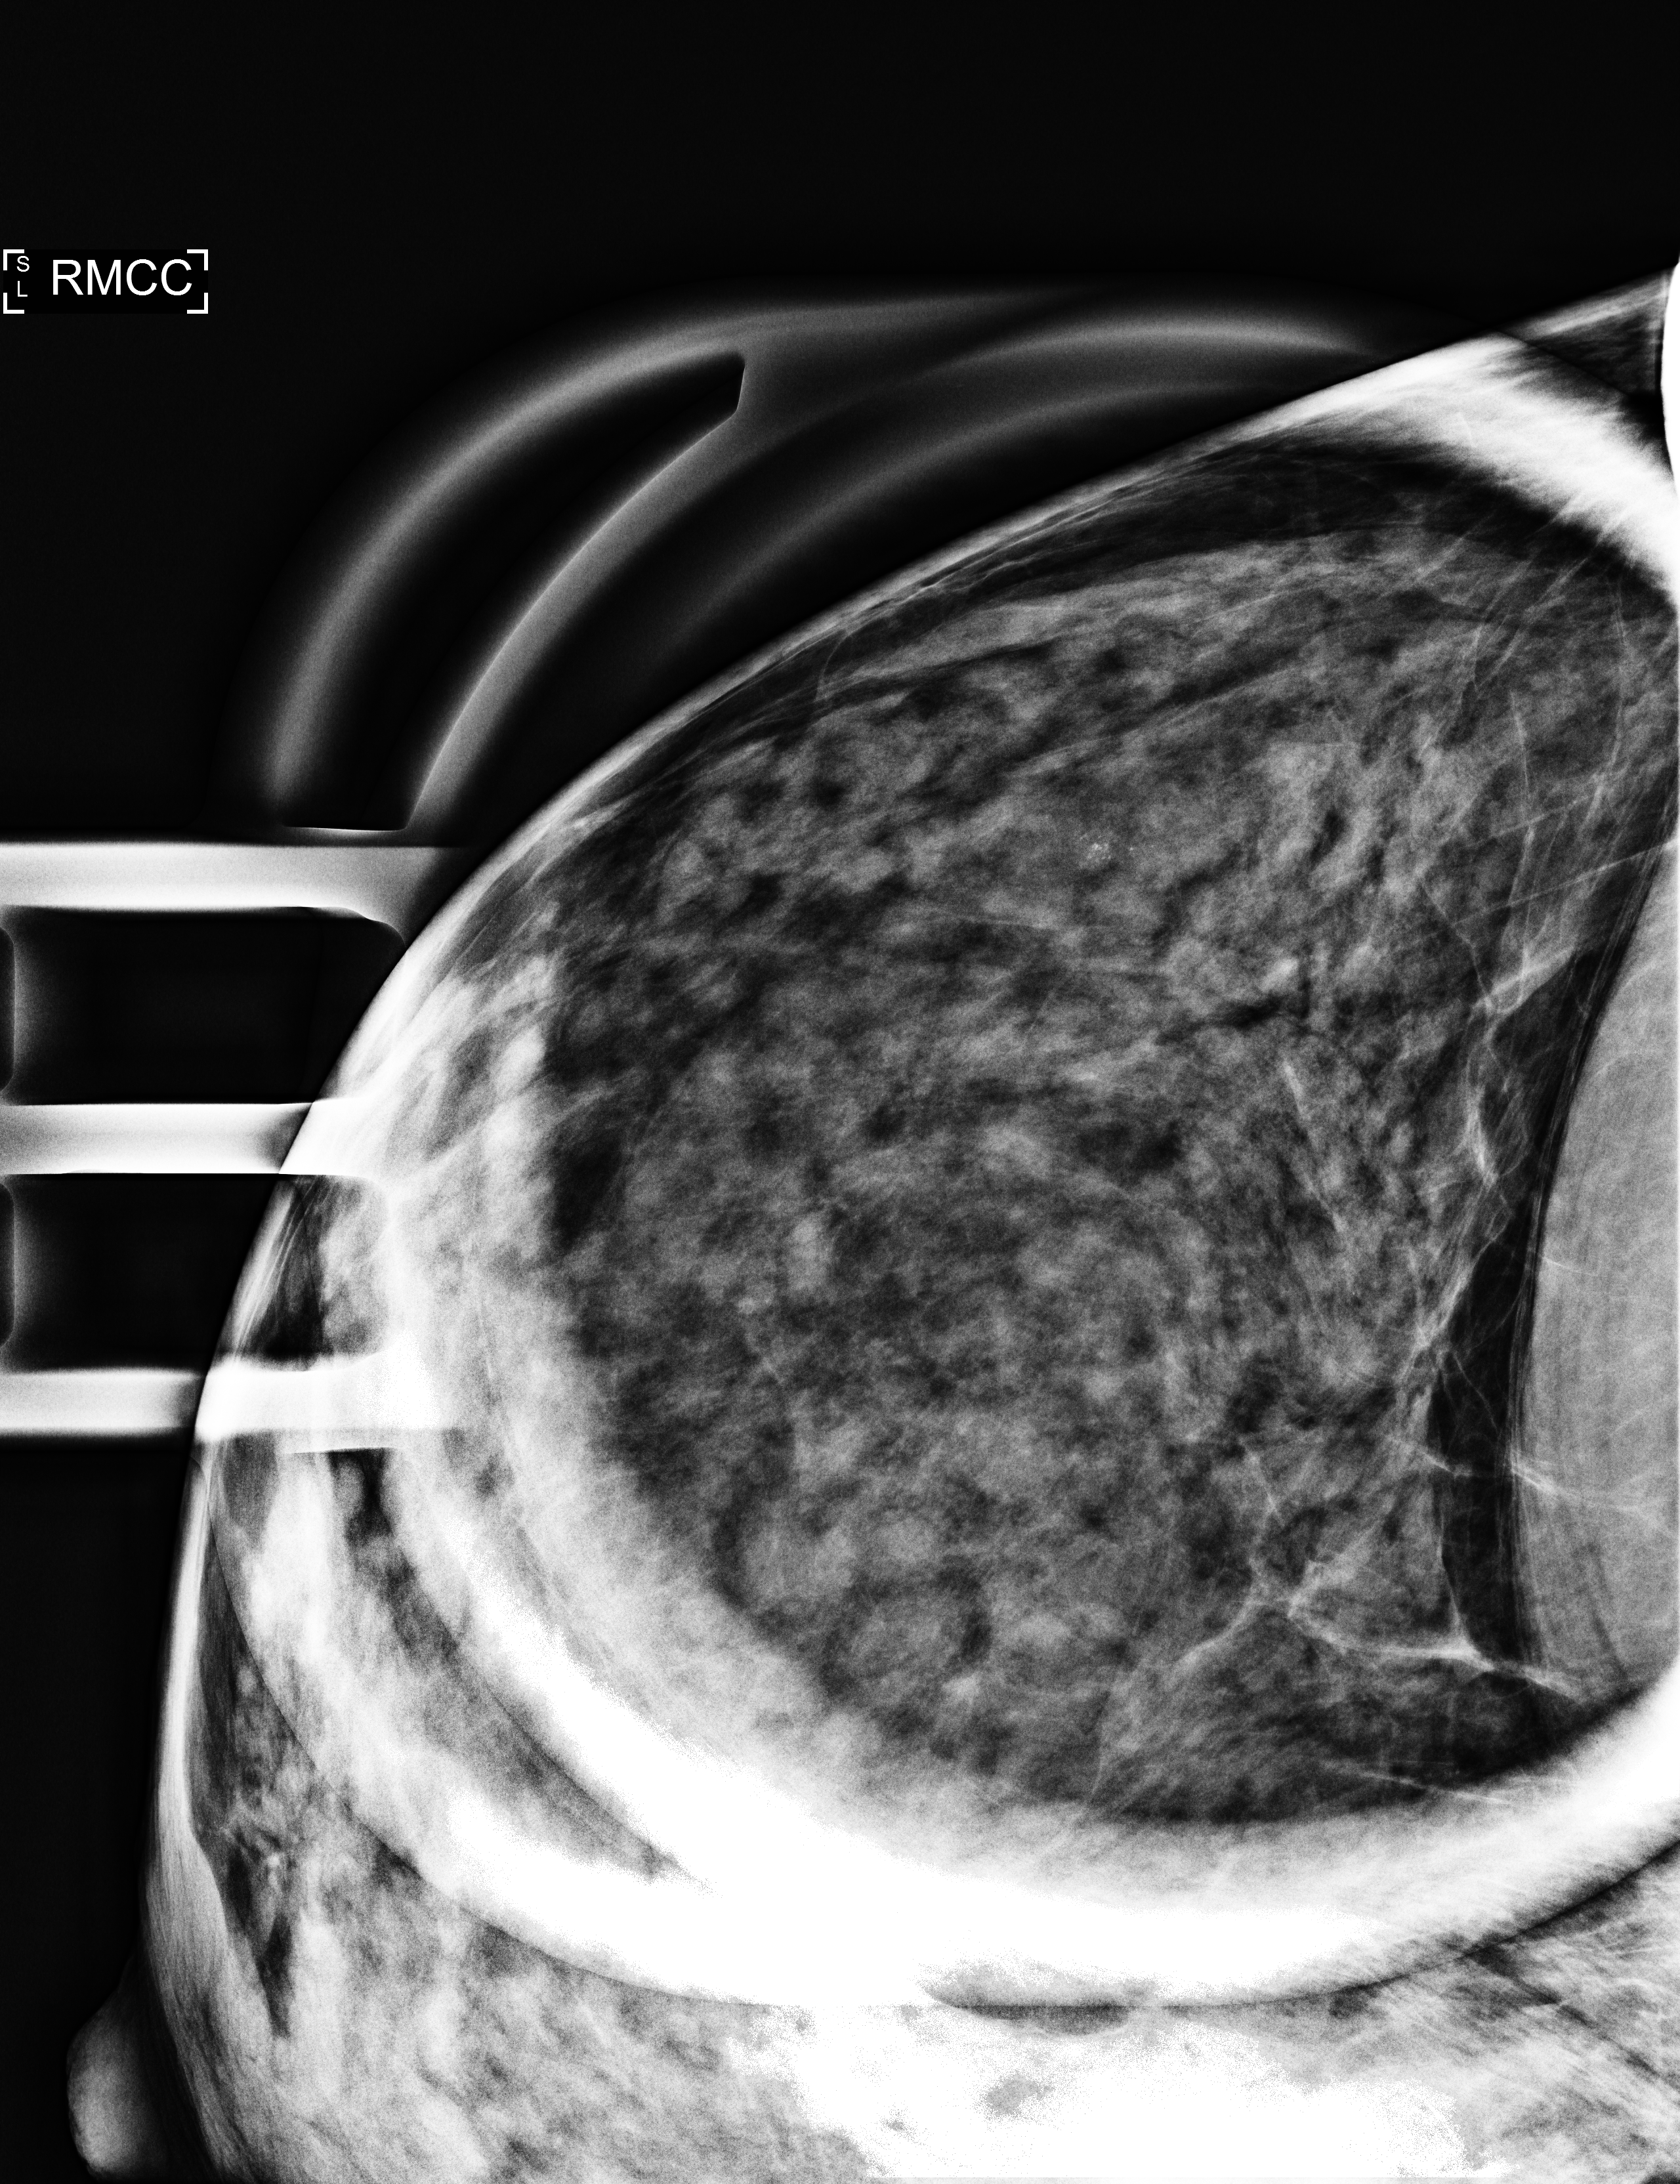
Additional work-up view. Patient: female, 45 years.
Image type: full-field digital mammogram. Breast: right. Projection: CC view, magnification.